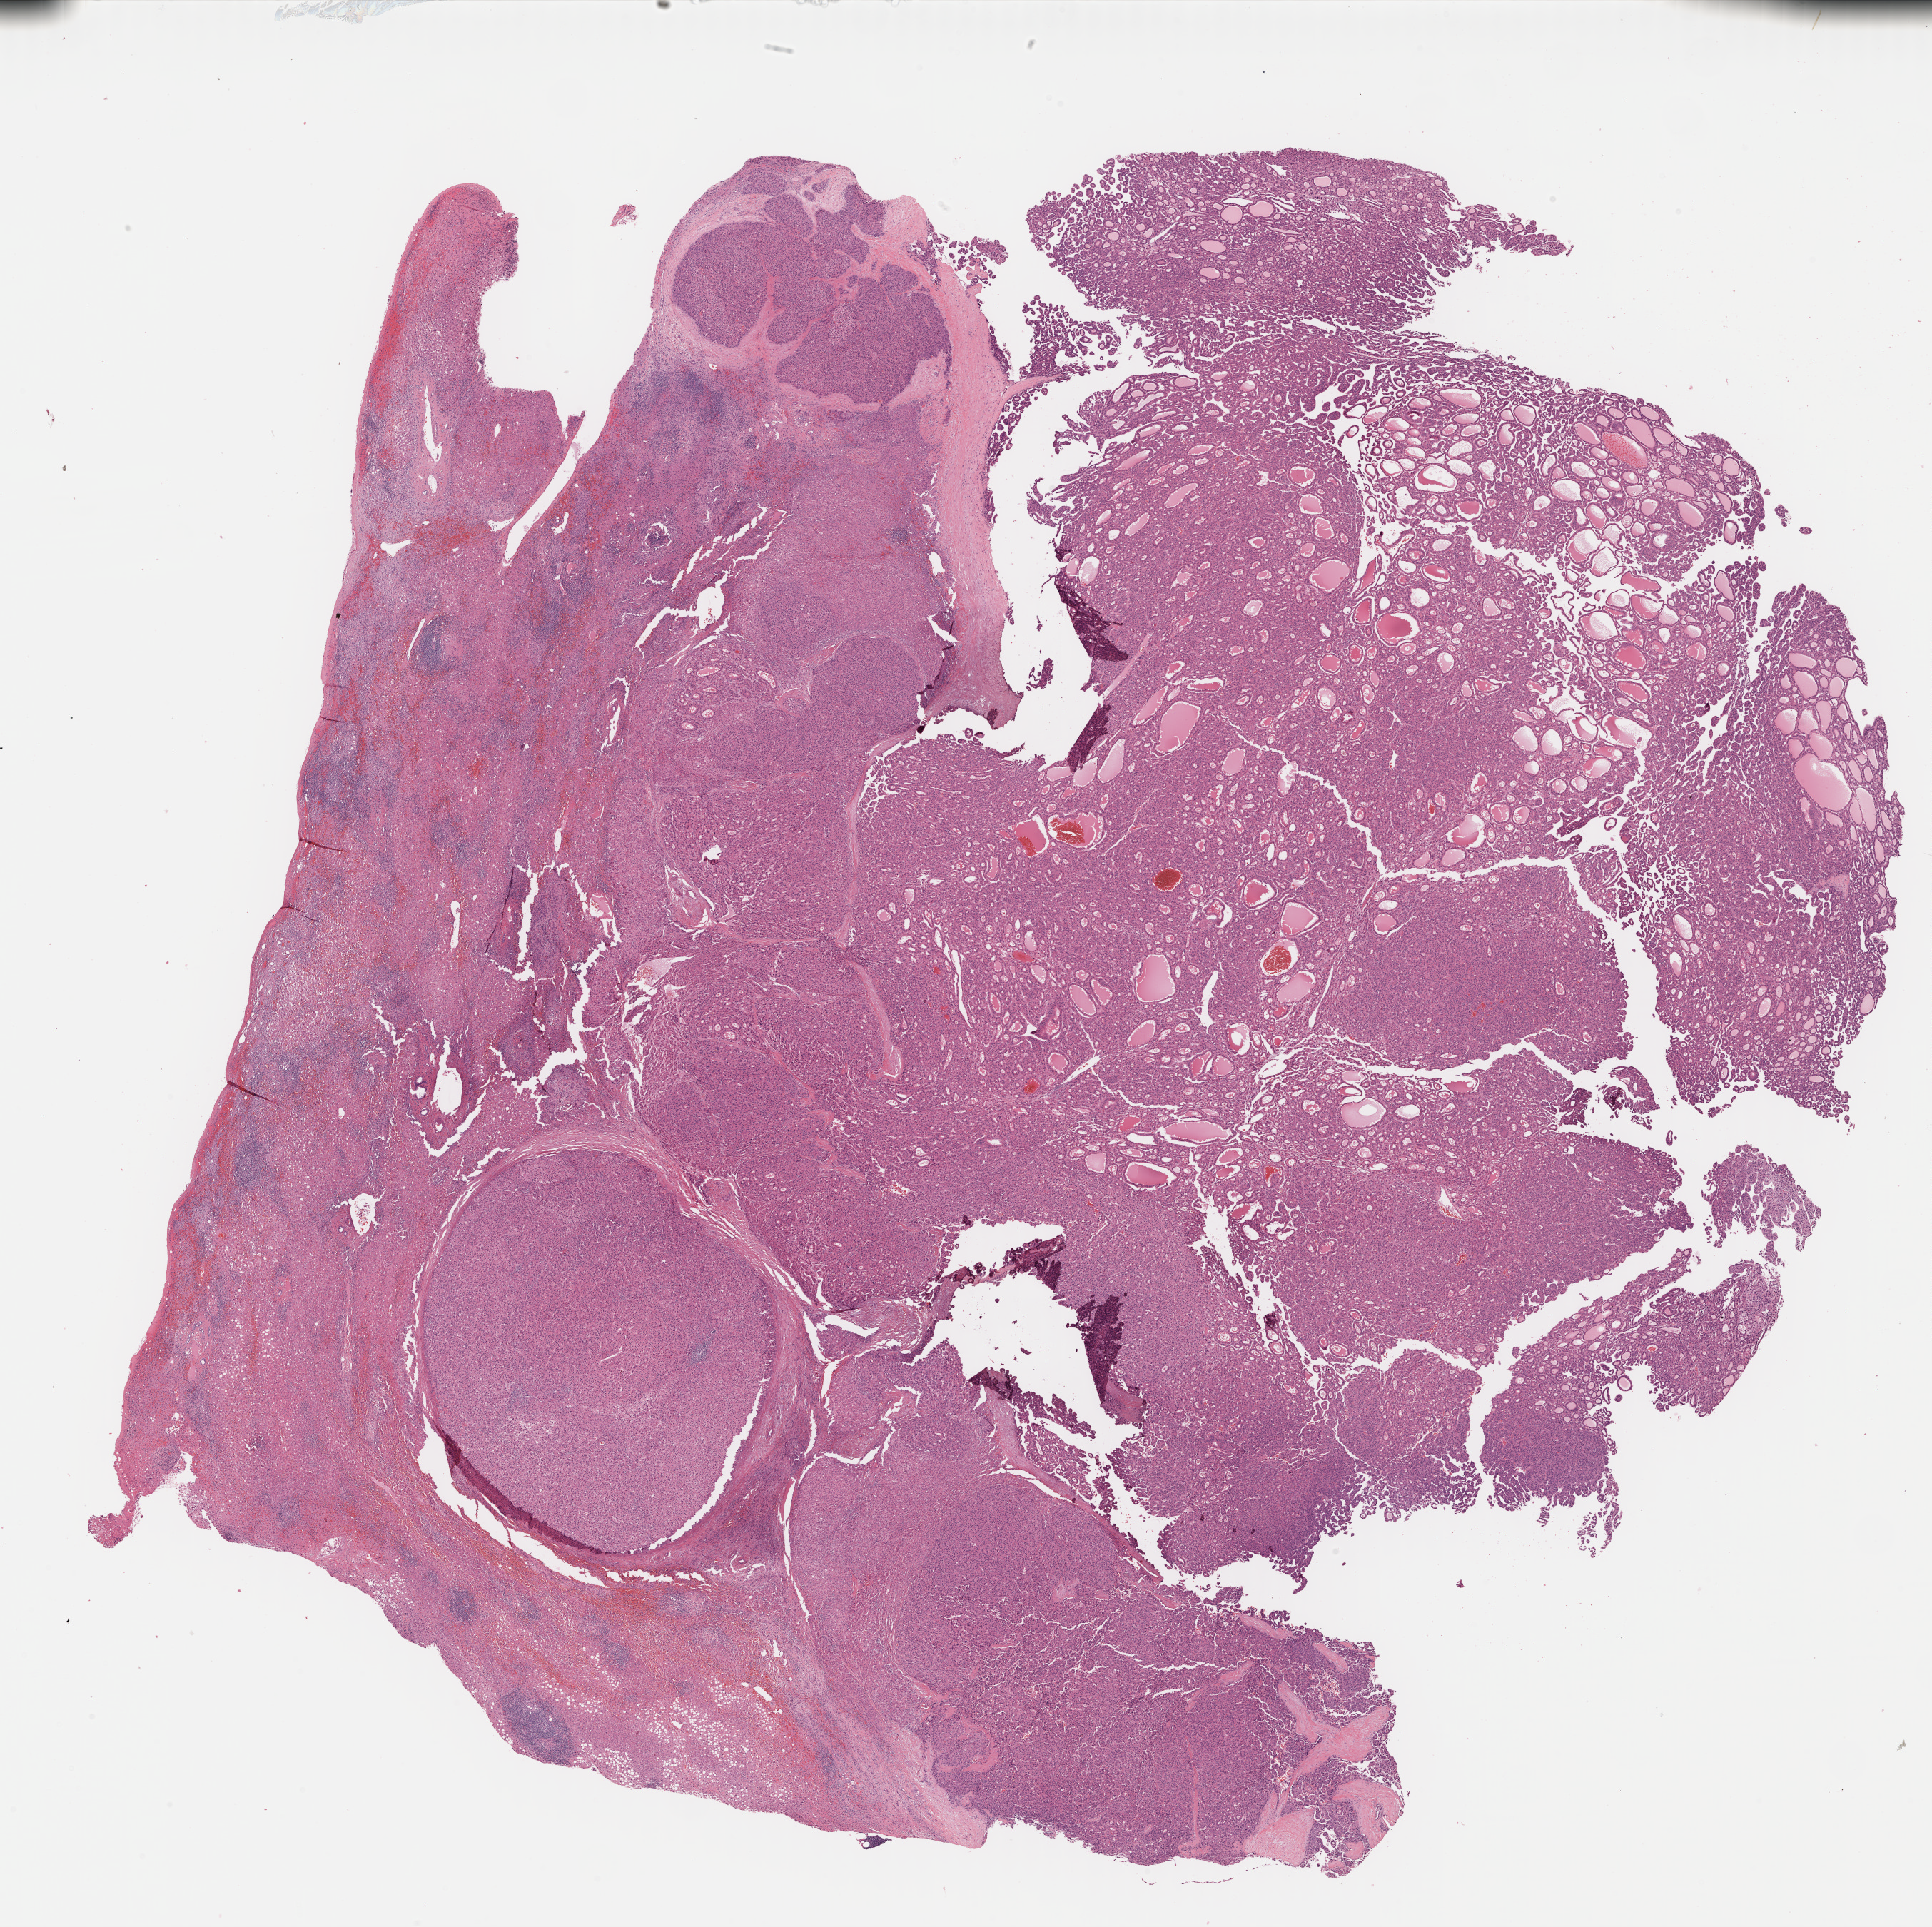
Digitized Hematoxylin and eosin (H&E) stained tissue section (whole slide), shown as a low-resolution overview of the whole scanned area (about 21.9 x 21.9 mm, slide scanned at 40x), FFPE section, sample: primary tumour, liver. Male patient; age at initial diagnosis 66 years. Histologic grade: G1 (well differentiated).
* diagnosis: Hepatocellular carcinoma, NOS
* TNM: T1 N0 M0
* AJCC pathologic stage: I (7th edition)